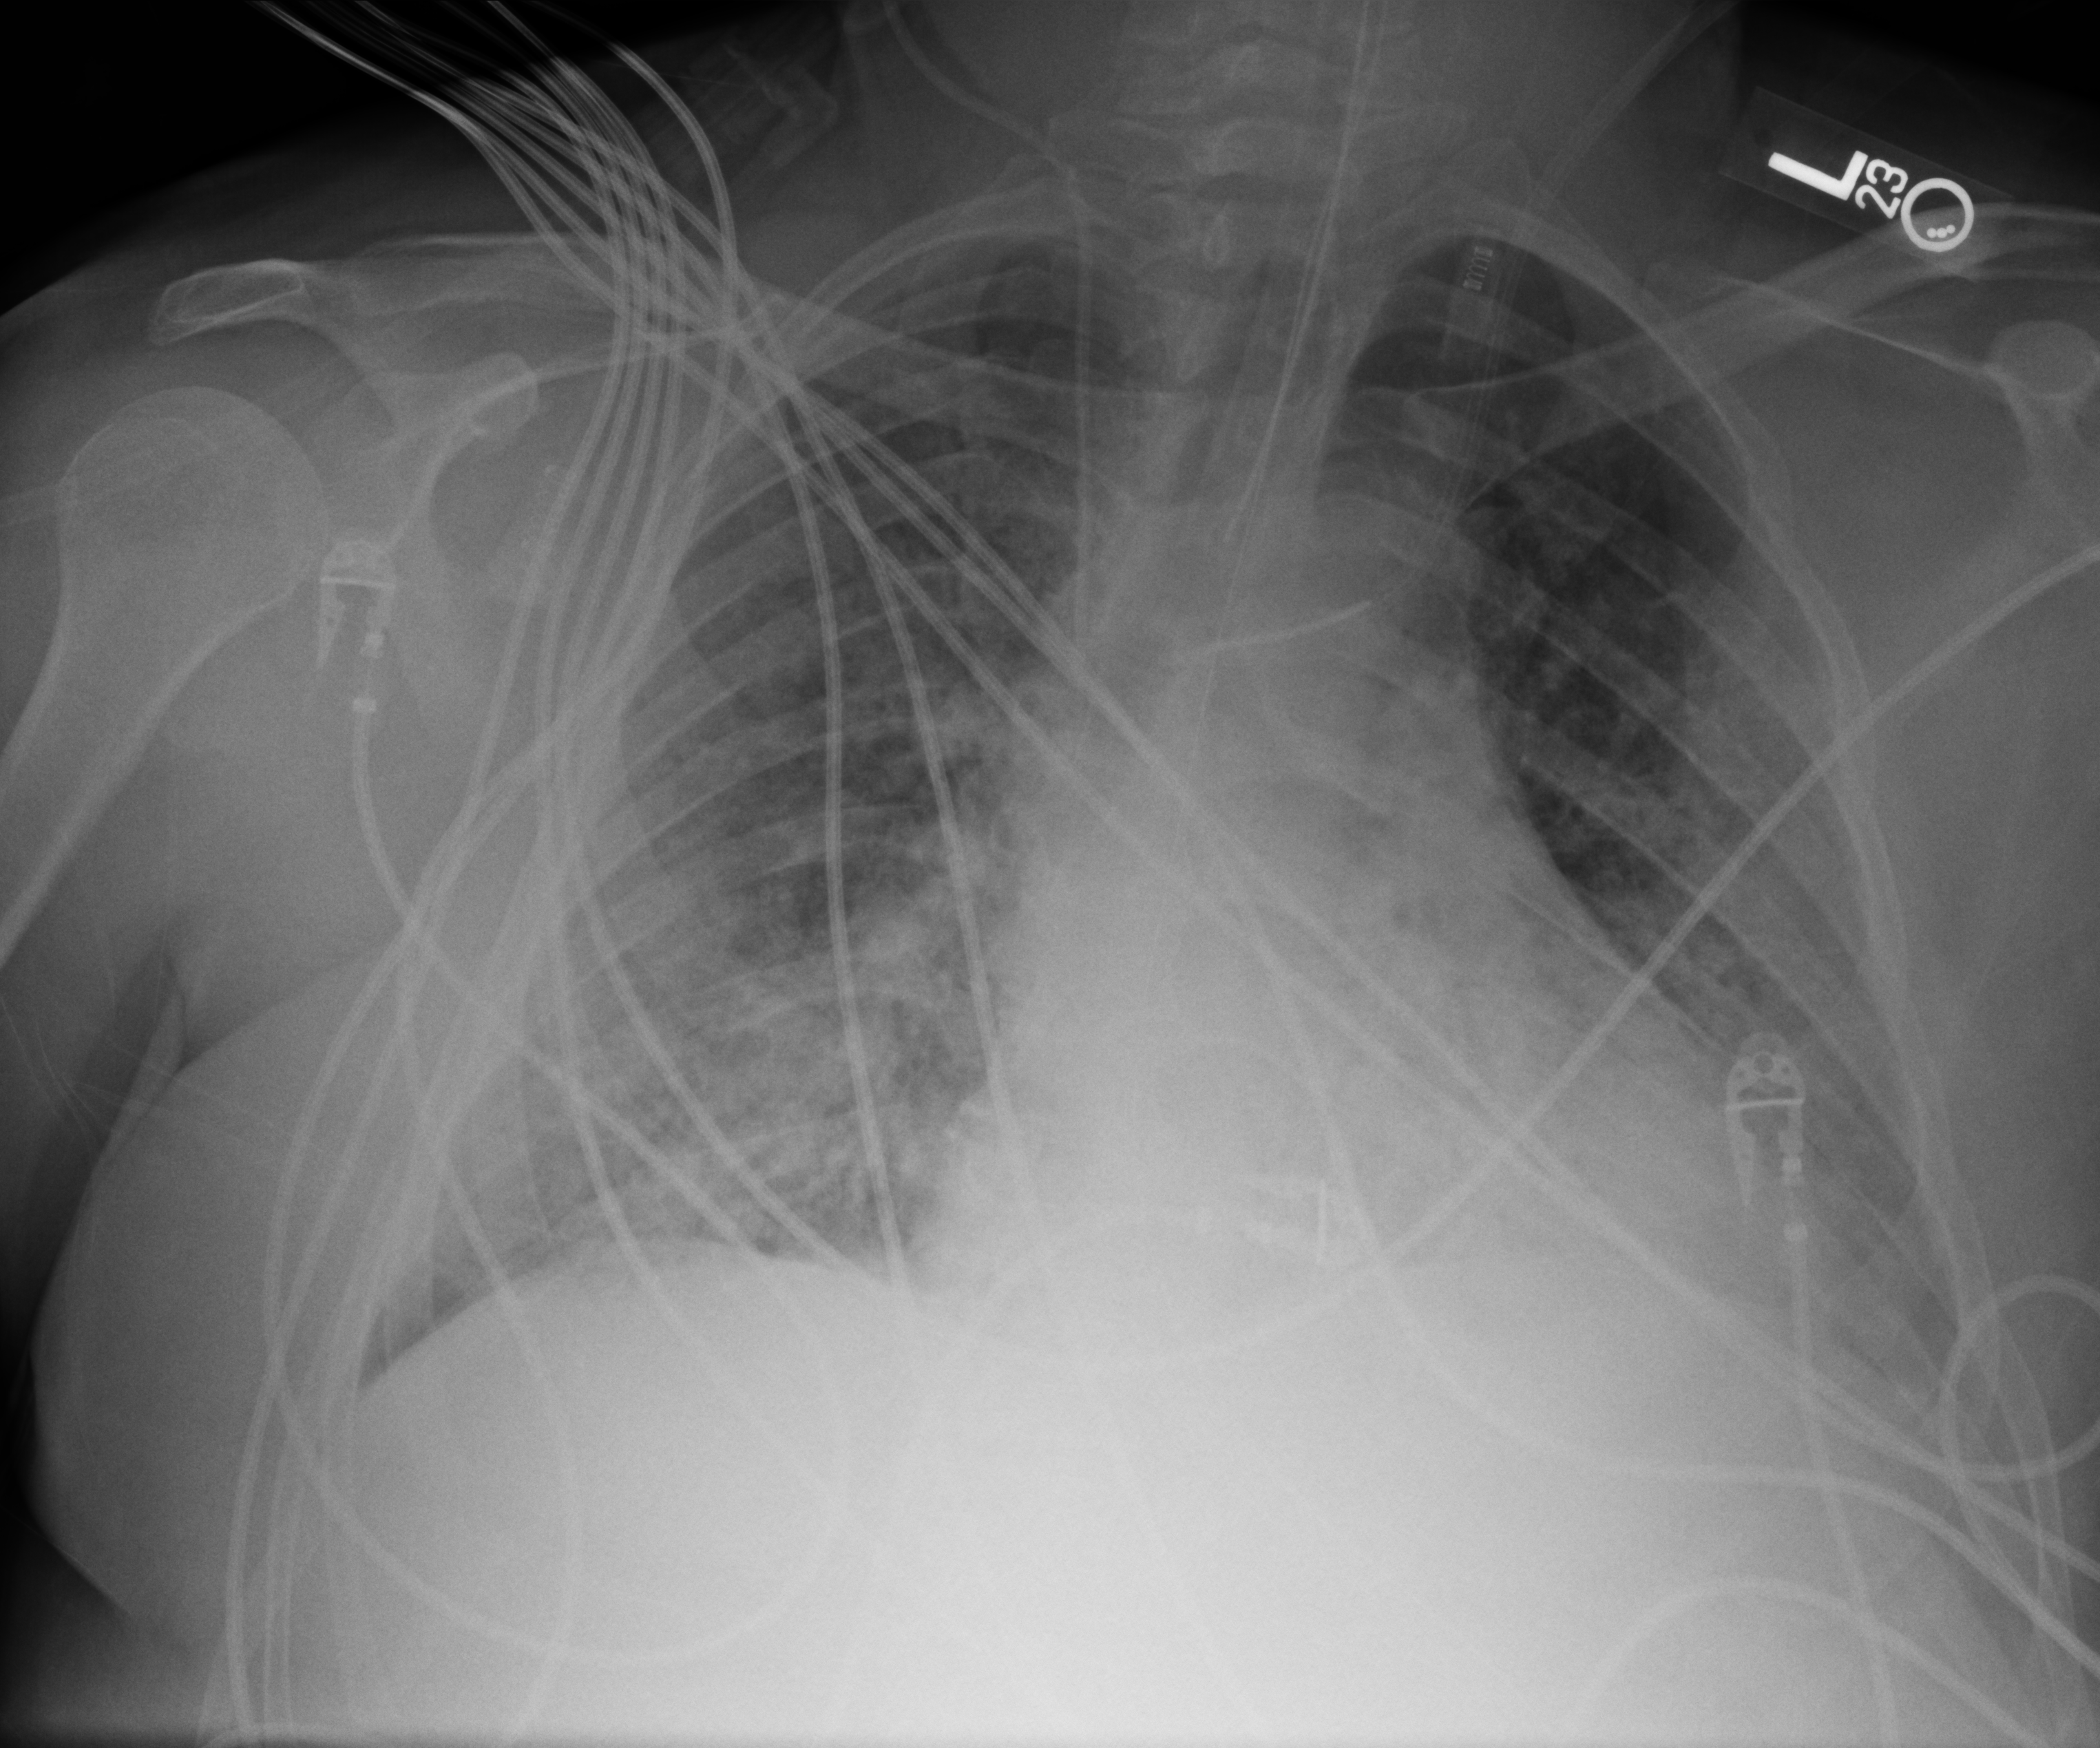
Portable chest radiograph, anteroposterior (AP) projection. Male patient hospitalised with COVID-19, age 18–59 years.
From the hospital-stay record, not from the radiograph (when in the stay this image was taken is not recorded): mechanically ventilated during this hospital stay: yes; length of hospital stay: 39 days.